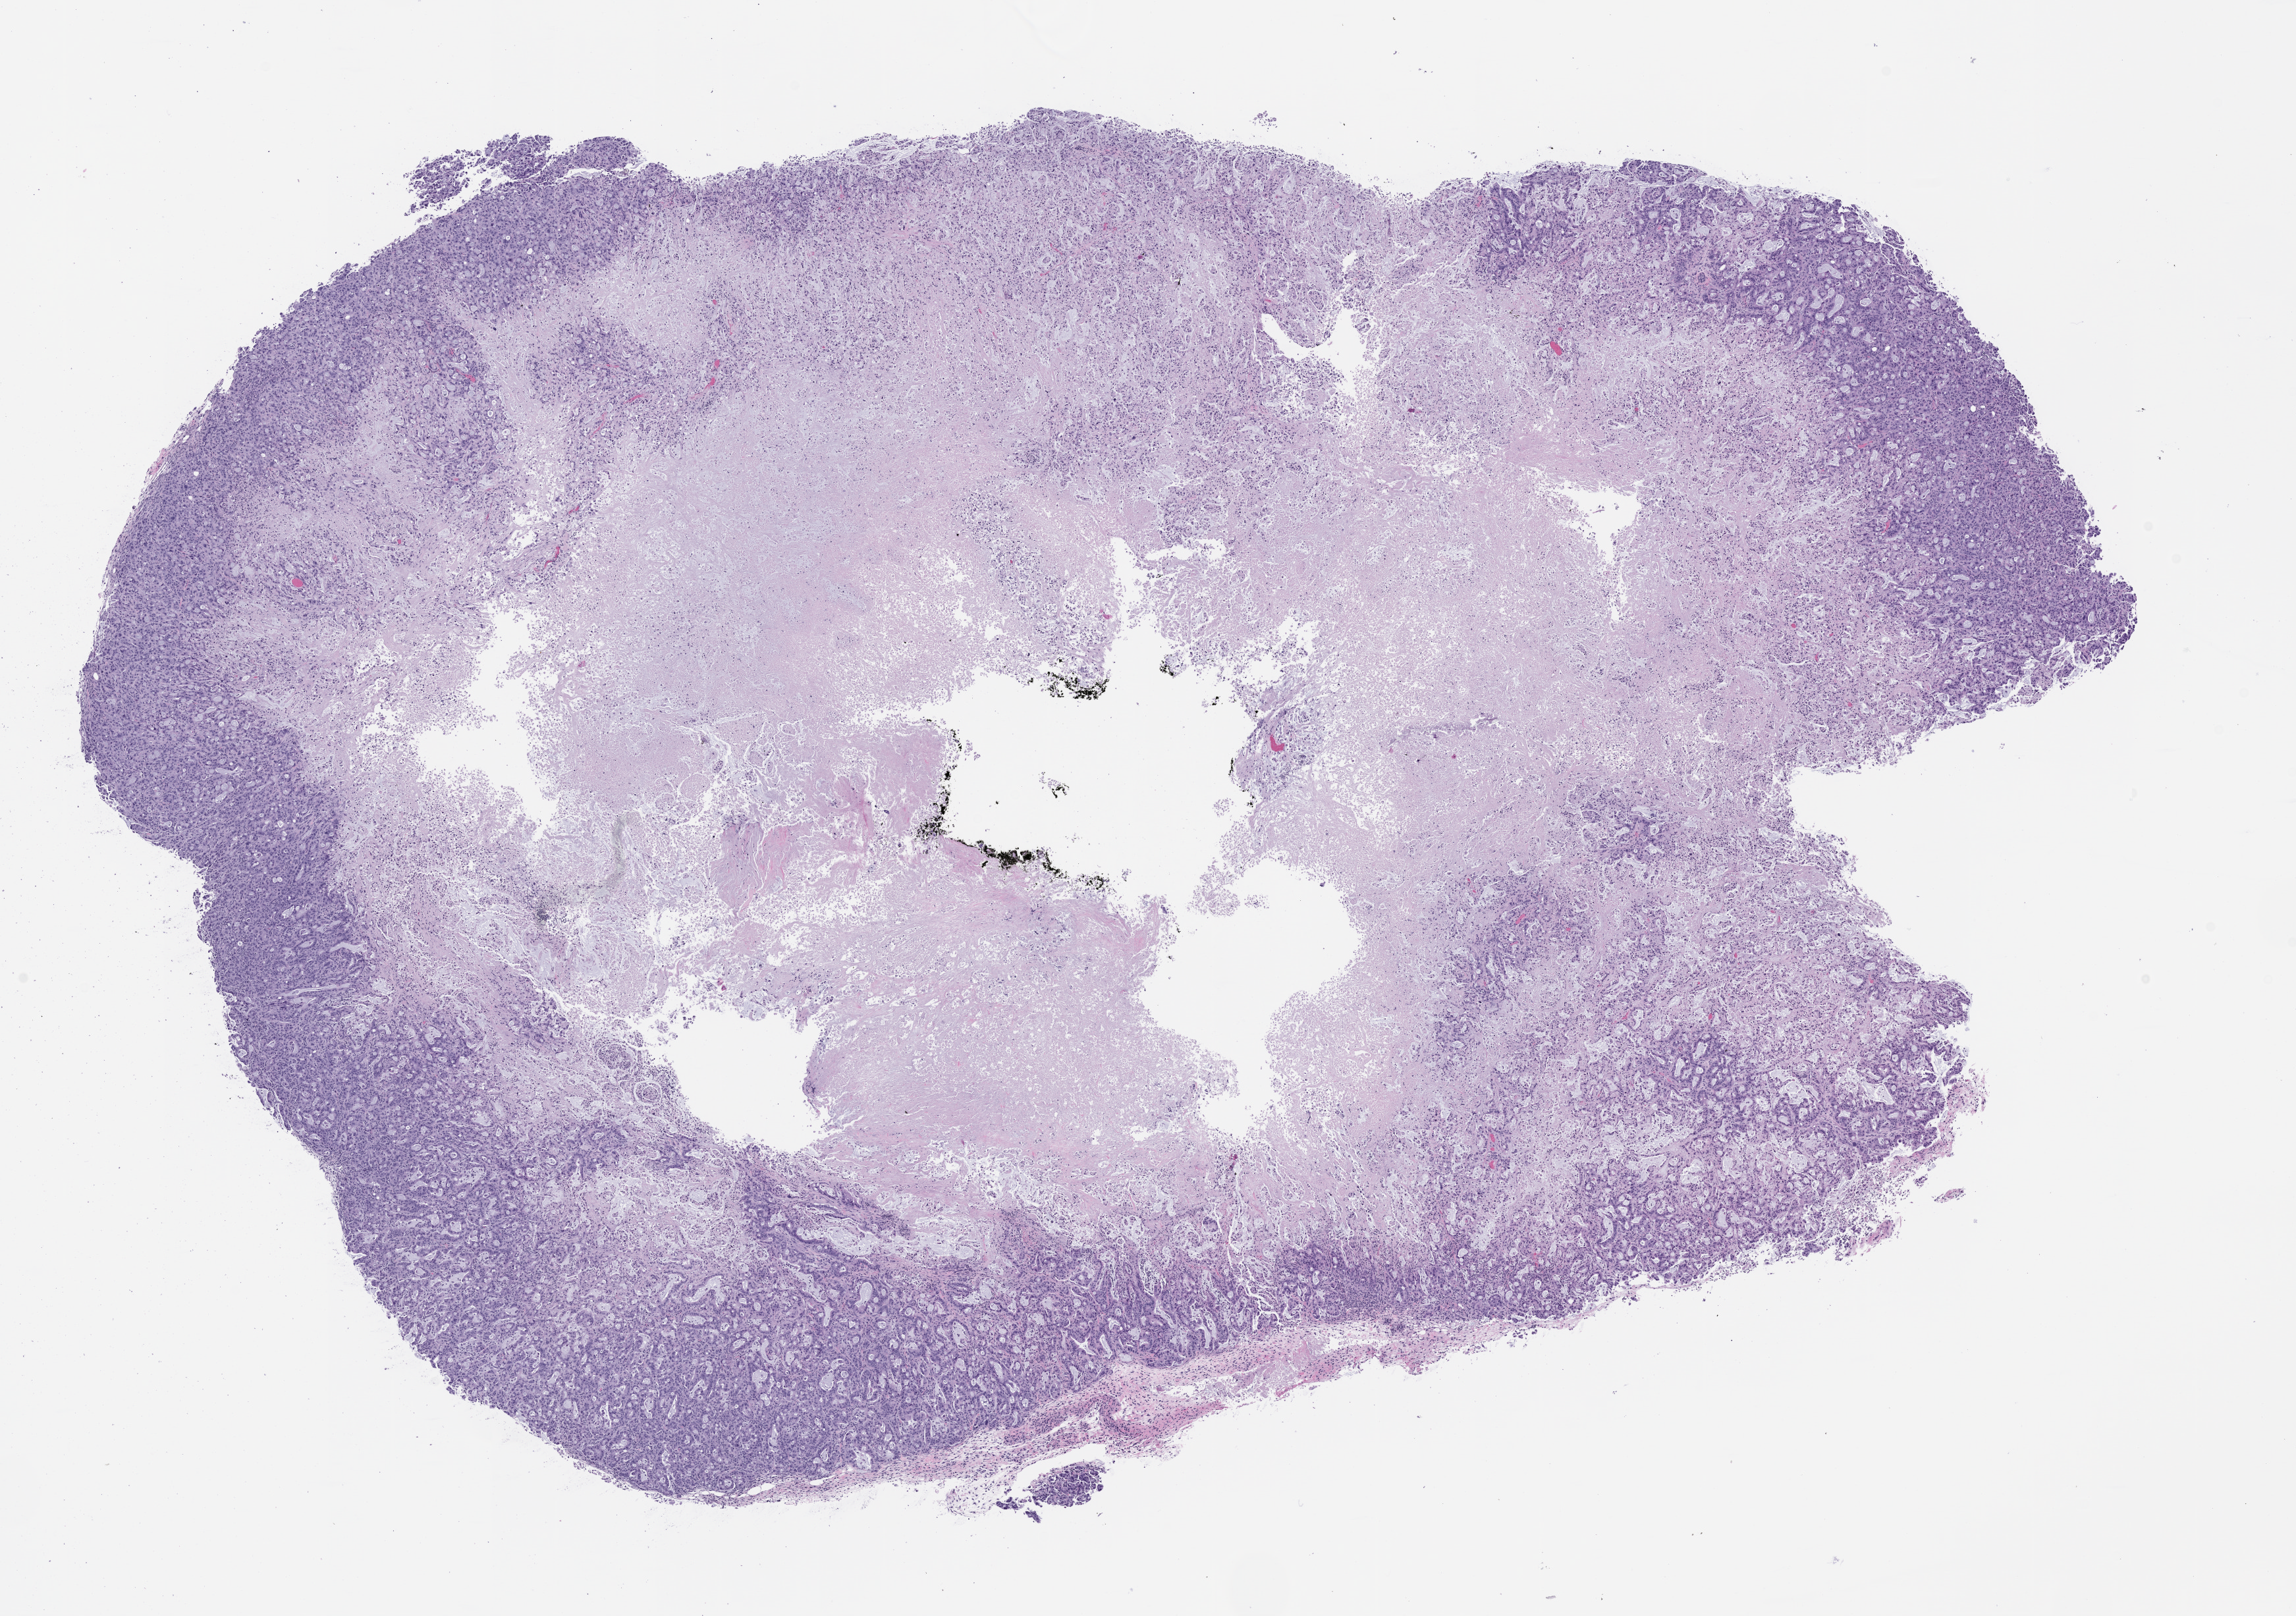
H&E whole-slide image of a patient-derived xenograft (PDX) tumor grown in a mouse, passage 1 — whole scanned area (about 14.0 x 9.9 mm) shown as a low-resolution overview, formalin-fixed, paraffin-embedded (FFPE) tissue, originating tumor site category: pancreas.
Originating patient diagnosis: Pancreatic Adenocarcinoma.